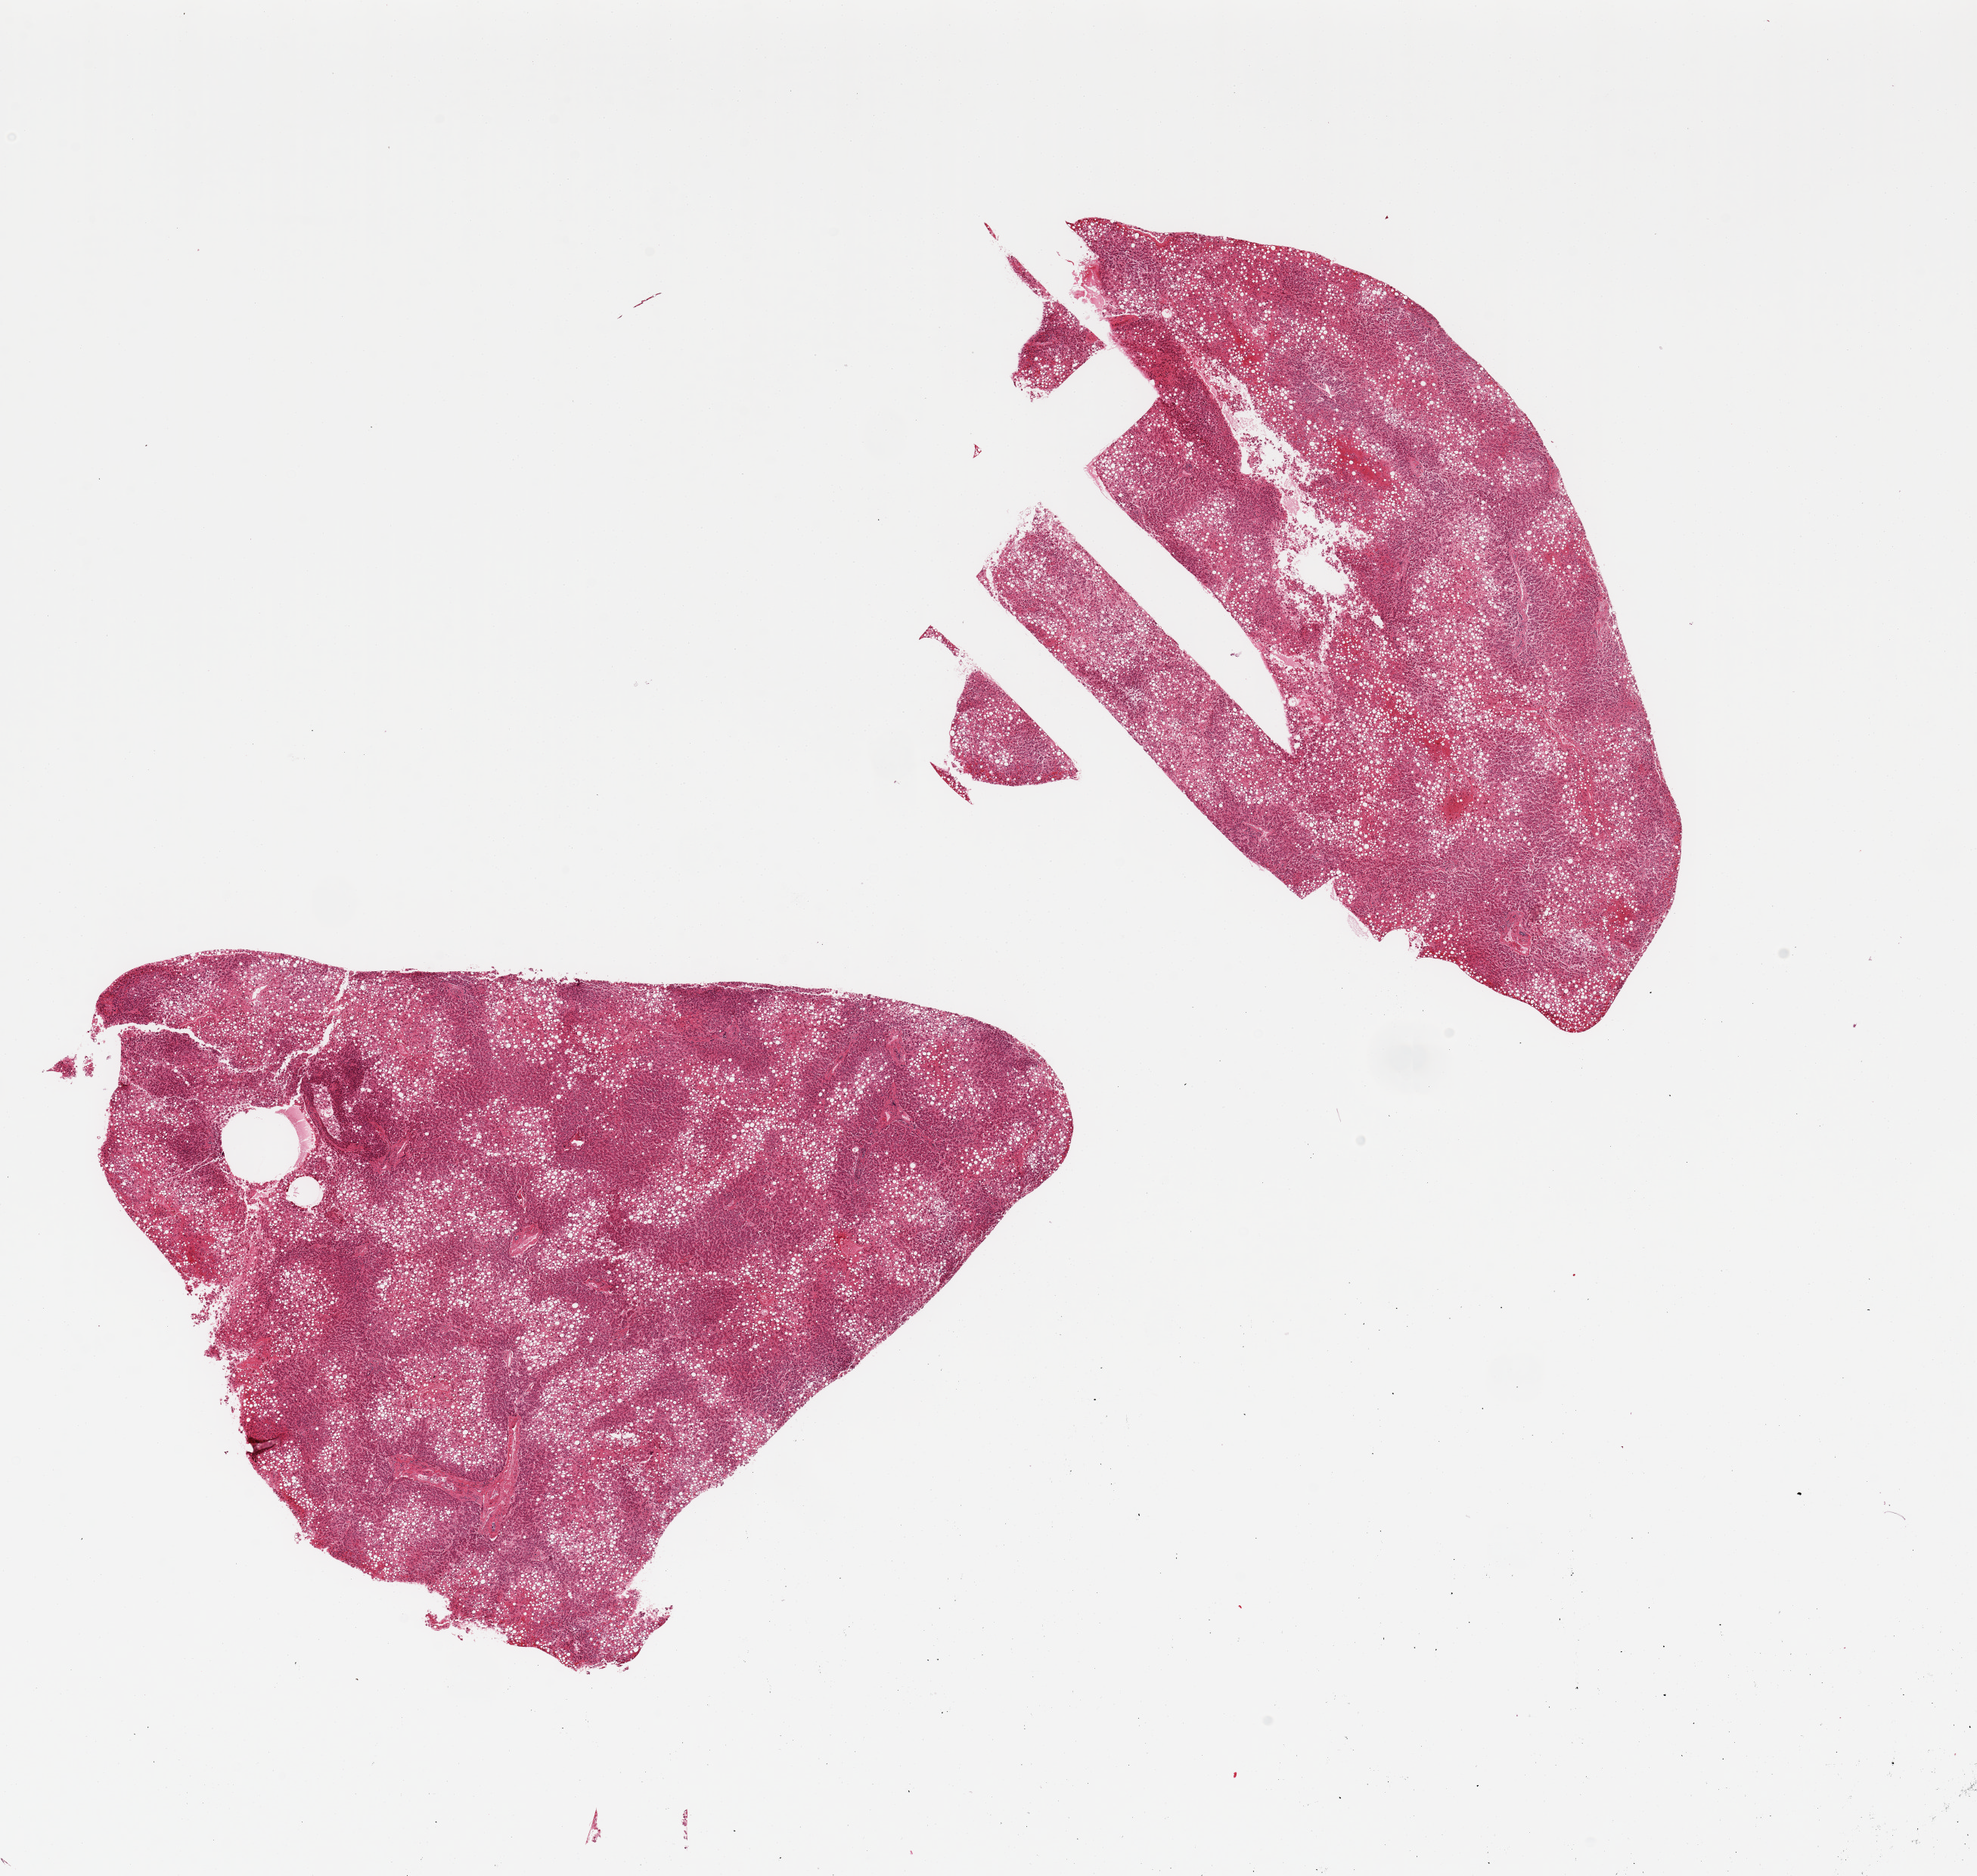
Whole-slide image, hematoxylin and eosin (H&E) stain — a low-resolution overview of the entire scanned area, about 20.7 x 19.6 mm (slide scanned at 20x), PAXgene-fixed, paraffin-embedded tissue, sampled site (target tissue): liver, donor tissue sample.
Review note (as recorded): 2 pieces; 50% macrovesicular steatosis.